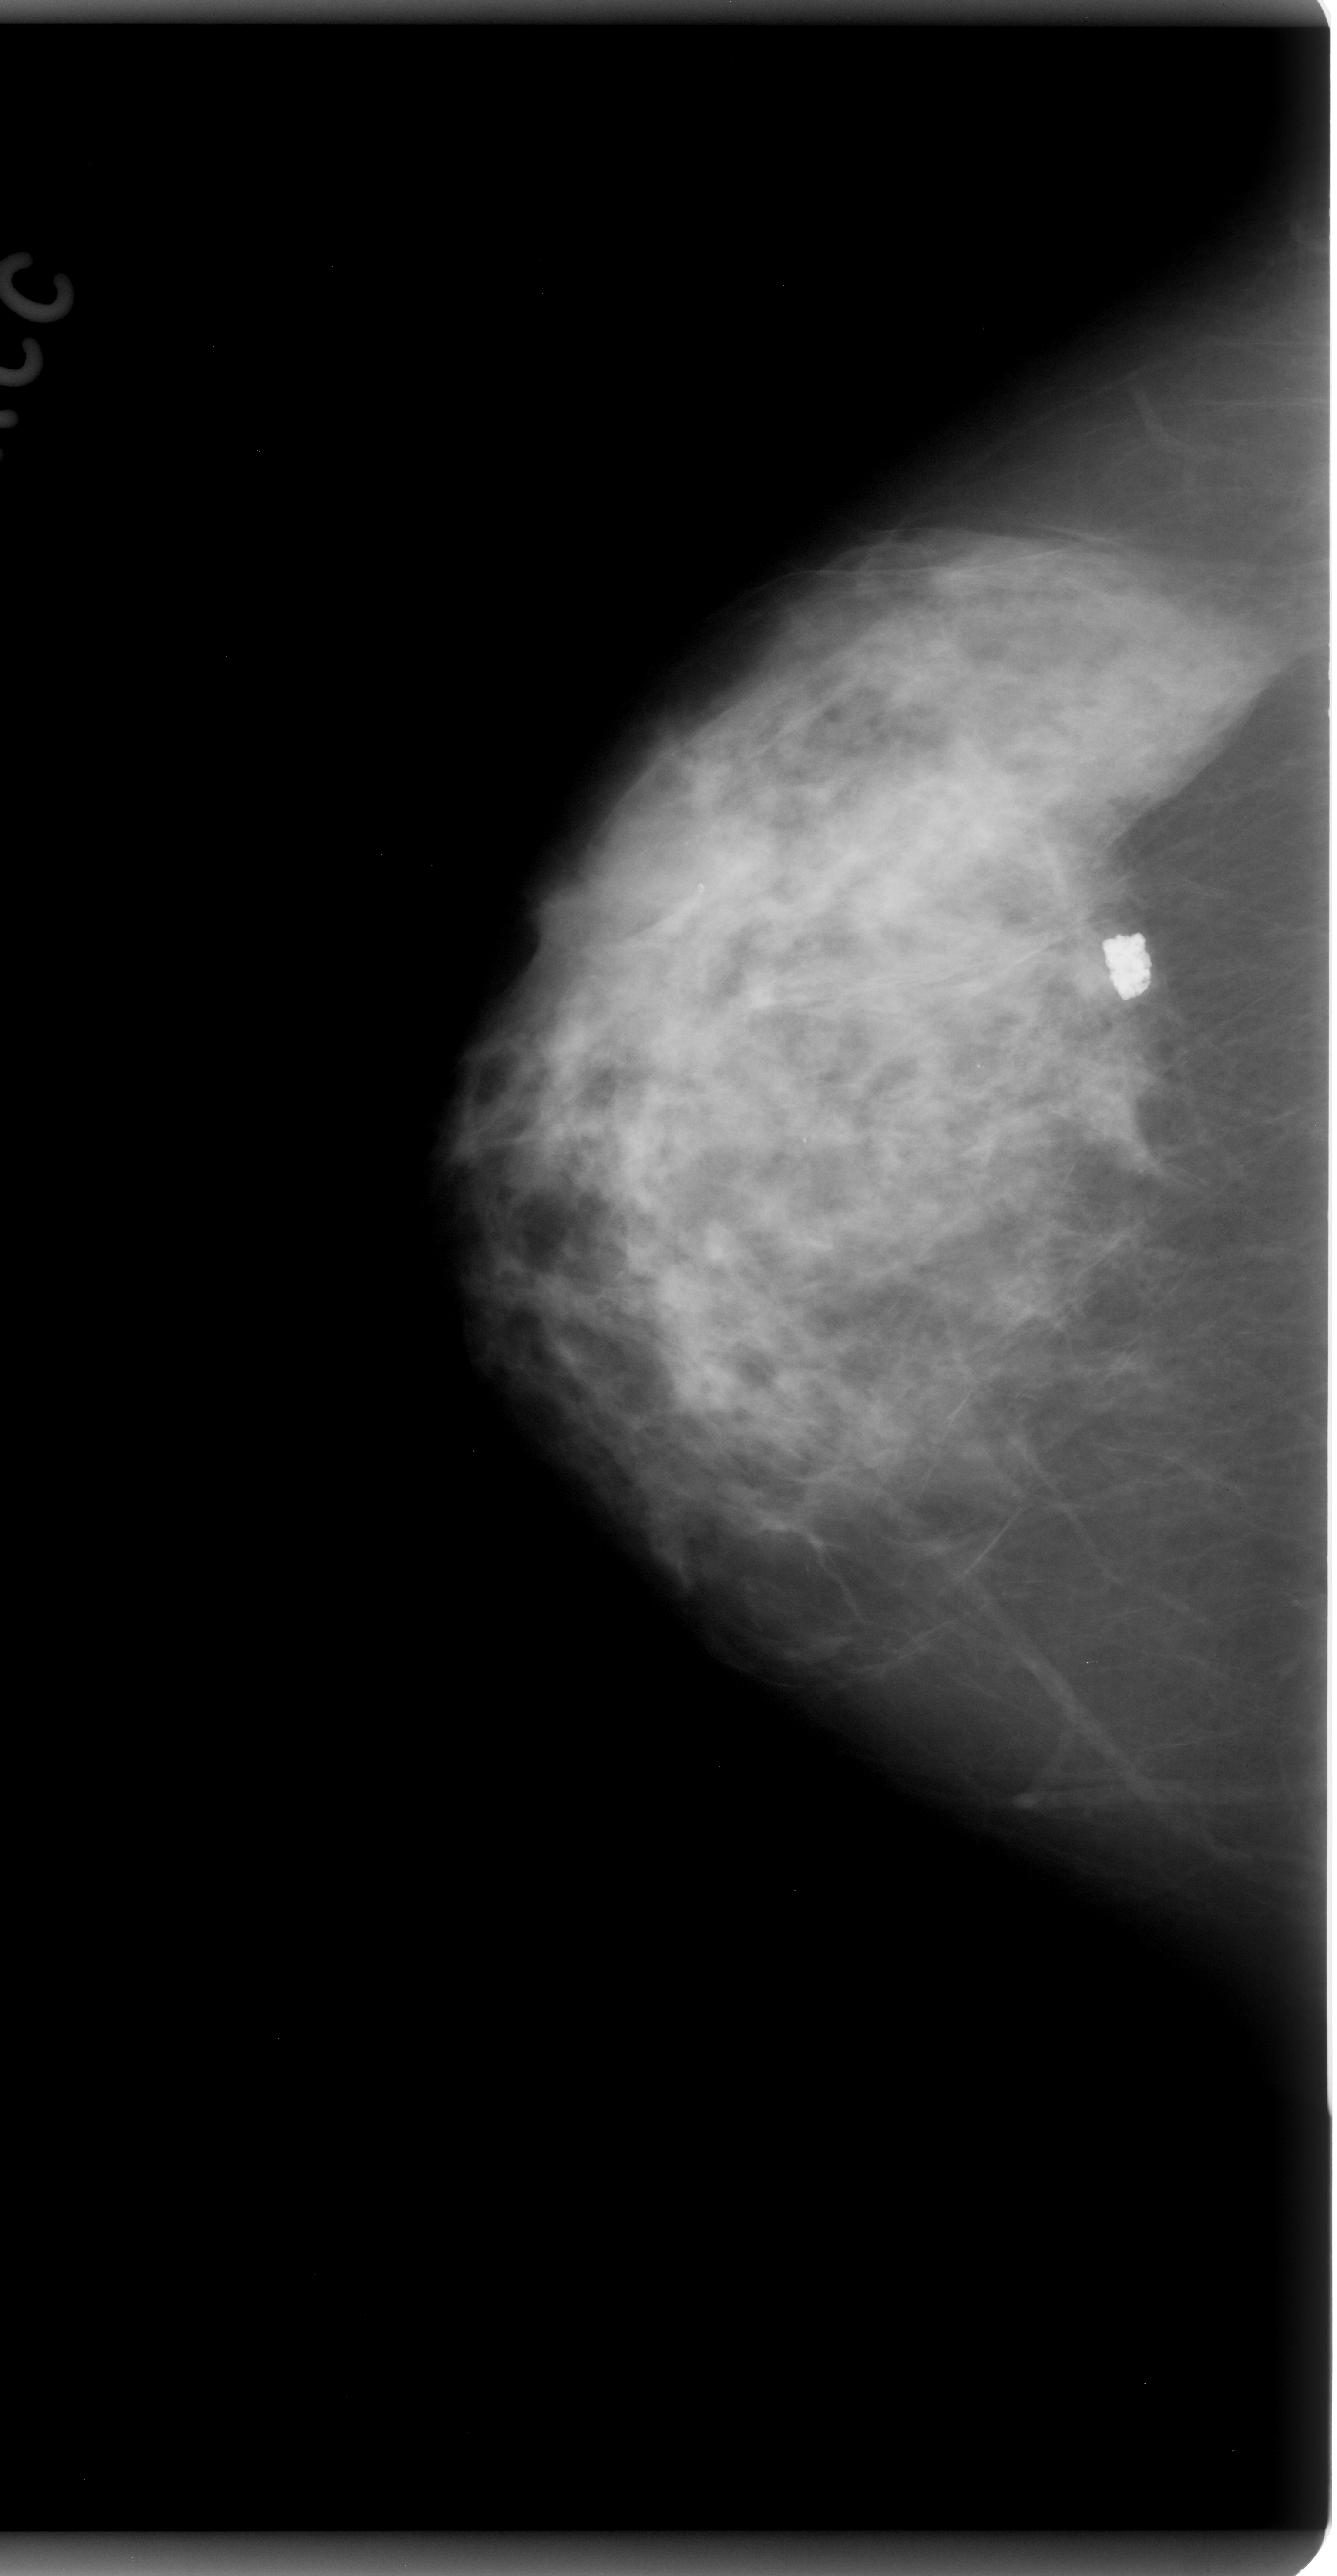
Scanned film-screen mammogram, right breast, CC view, breast composition: heterogeneously dense (BI-RADS density category 3 of 4).
- Marked abnormality: mass, shape irregular, margins spiculated; BI-RADS assessment category 5; pathology result (as recorded, not read from the image): malignant.